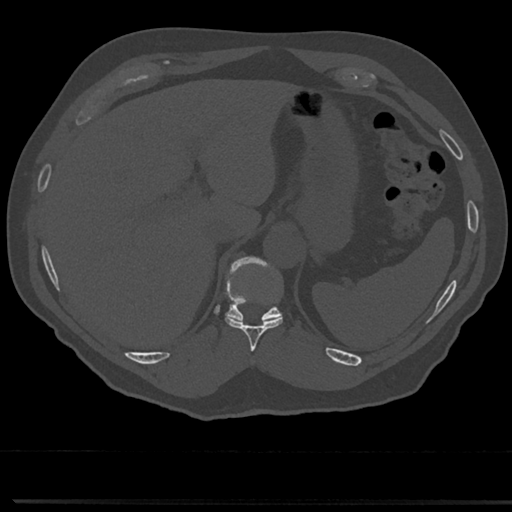
CT including the spine, one axial slice. Slice 236 of 817 in the series (ordered by position). 120 kVp. Bone window (W 1800 / L 400 HU). 0.5 mm slice thickness. 512 × 512 image matrix, field of view 355 × 355 mm. Patient: male, 61 years. Case-level facts recorded for this patient, not image findings: primary cancer: prostate.
Outlined on this slice (semi-automatically segmented with operator editing):
- T10 vertebra: bounding box (x1, y1, x2, y2) in pixels: (225, 273, 283, 349)
- T11 vertebra: (227, 260, 281, 322)